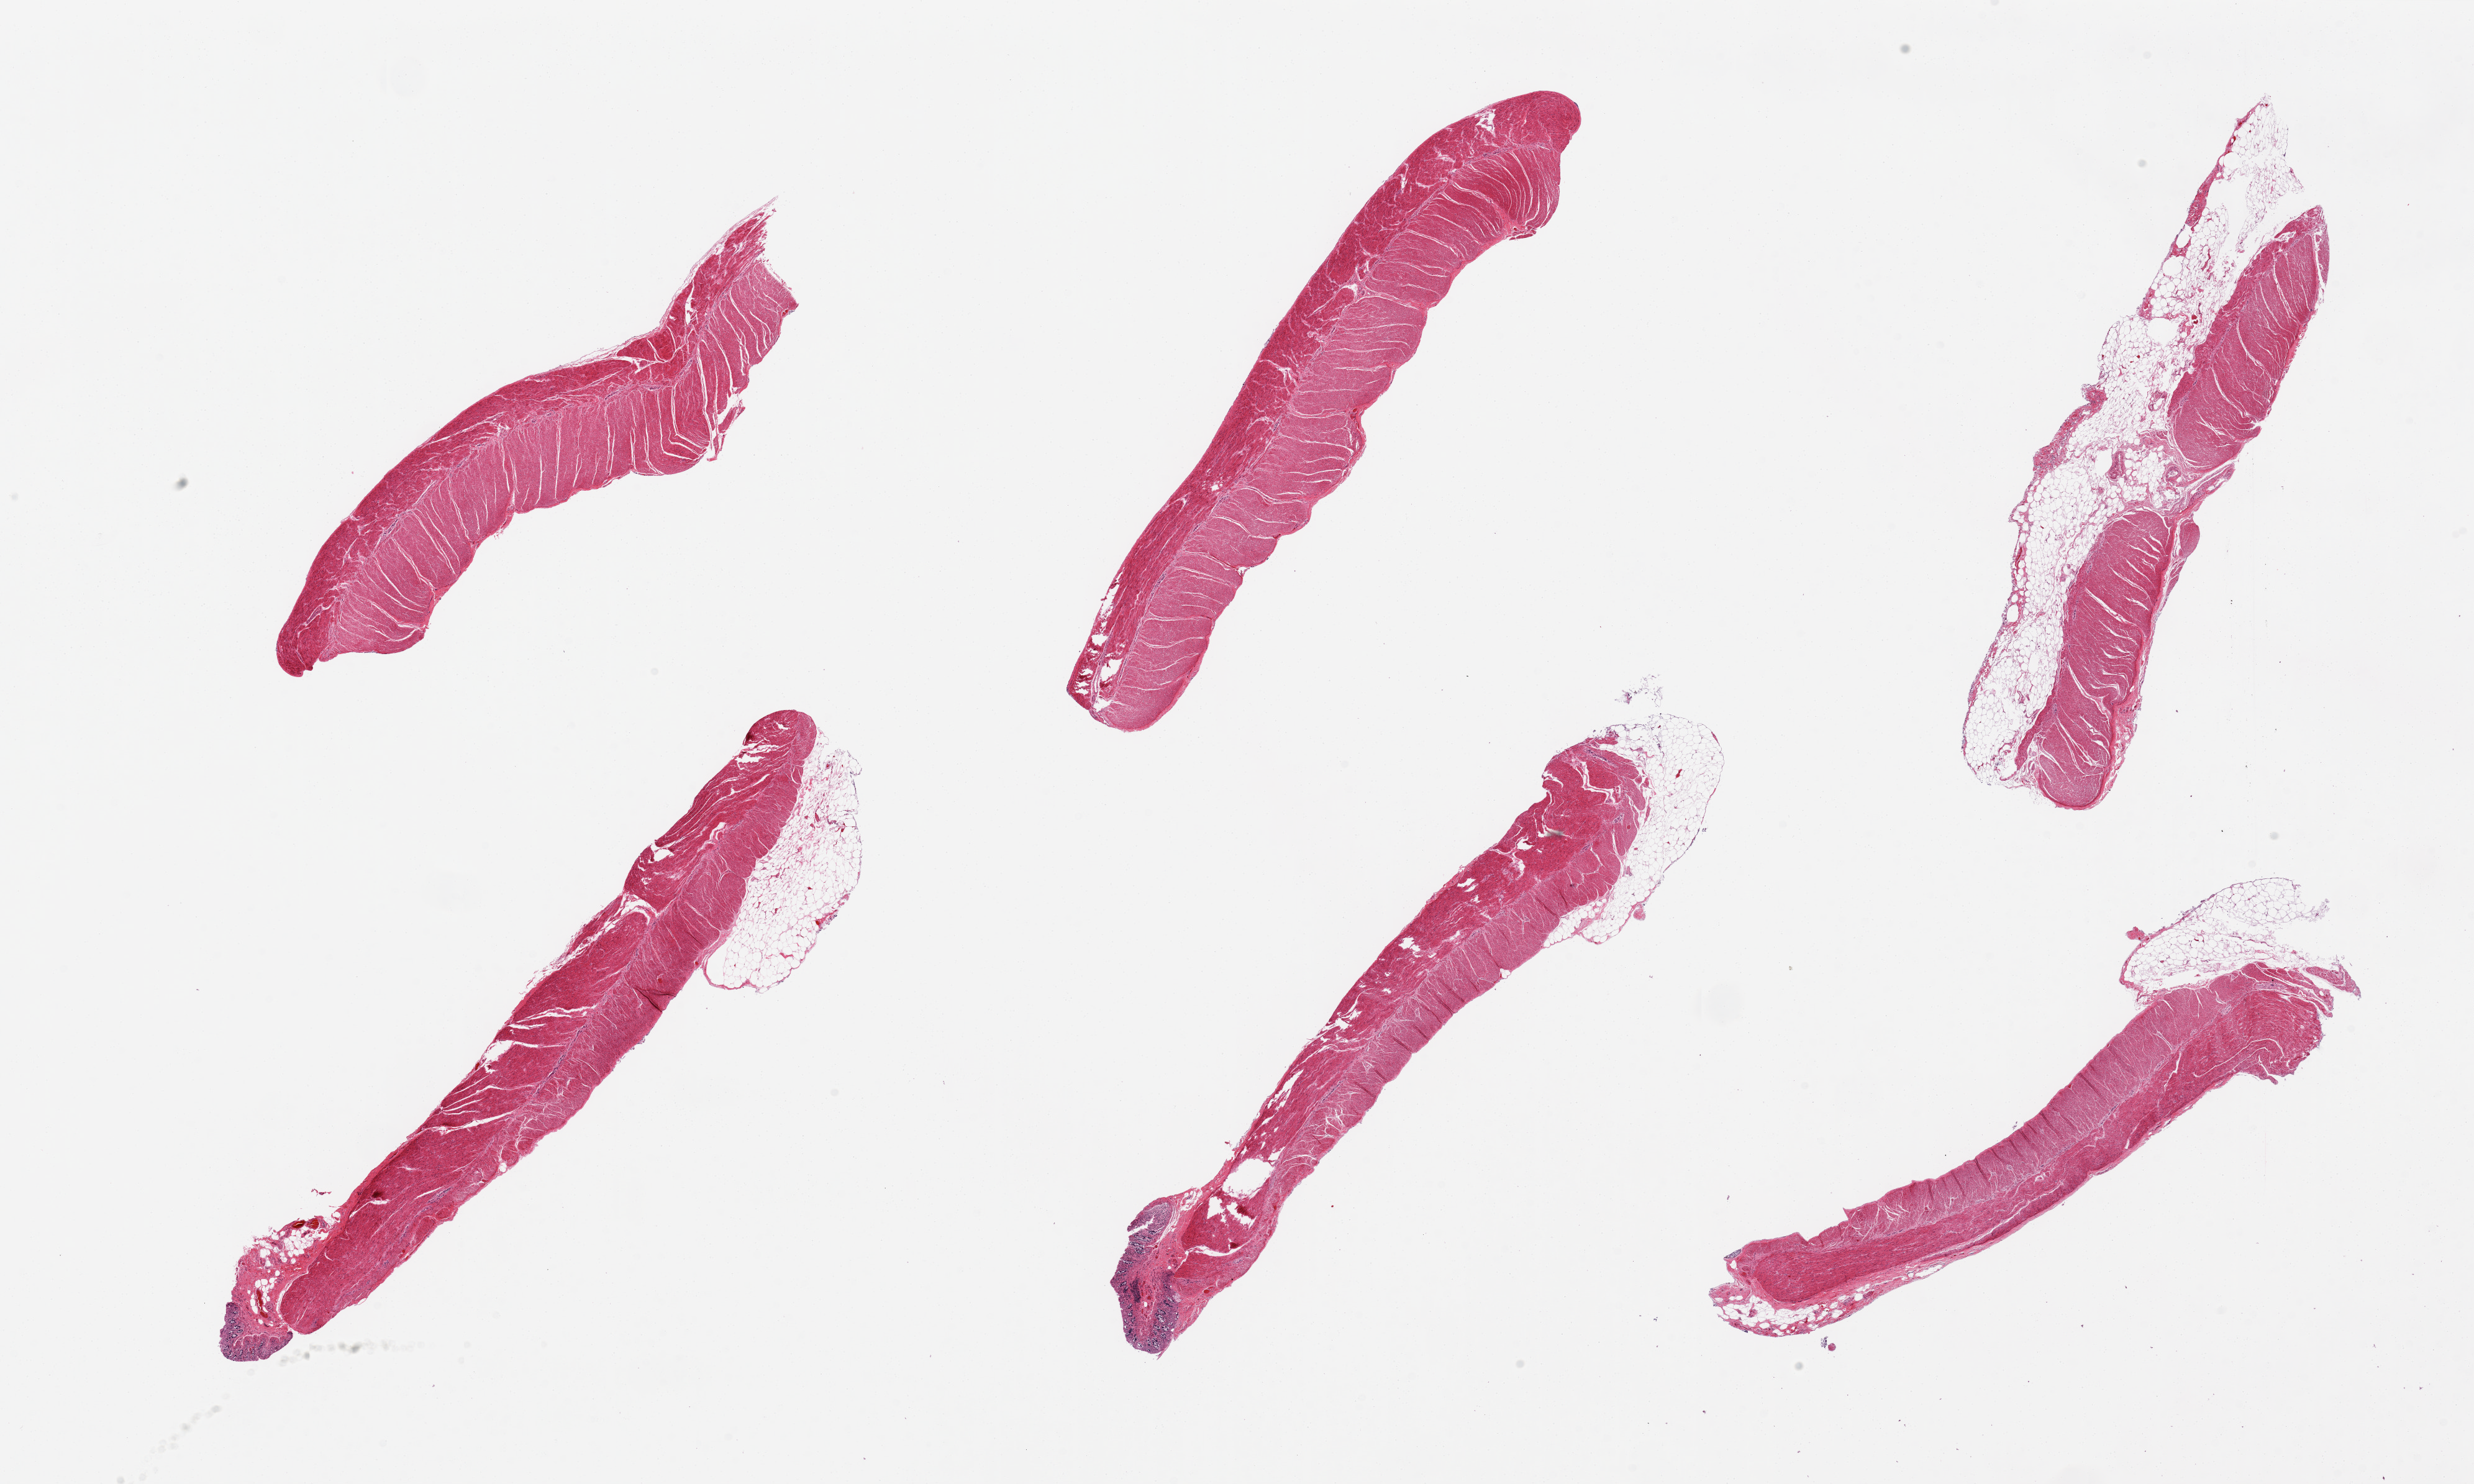
Digitized hematoxylin and eosin (H&E)-stained section, brightfield — a low-resolution overview of the entire scanned area, about 31.5 x 18.9 mm. PAXgene-fixed paraffin-embedded (PFPE) section. Section of sigmoid colon (target tissue). Tissue donor sample. Male donor.
- pathologist's review note for this sample: 6 pieces, muscularis present (target); few pieces include 10 to 40% fat up to 1.175 mm; two pieces with small fragments of autolyzed mucosa